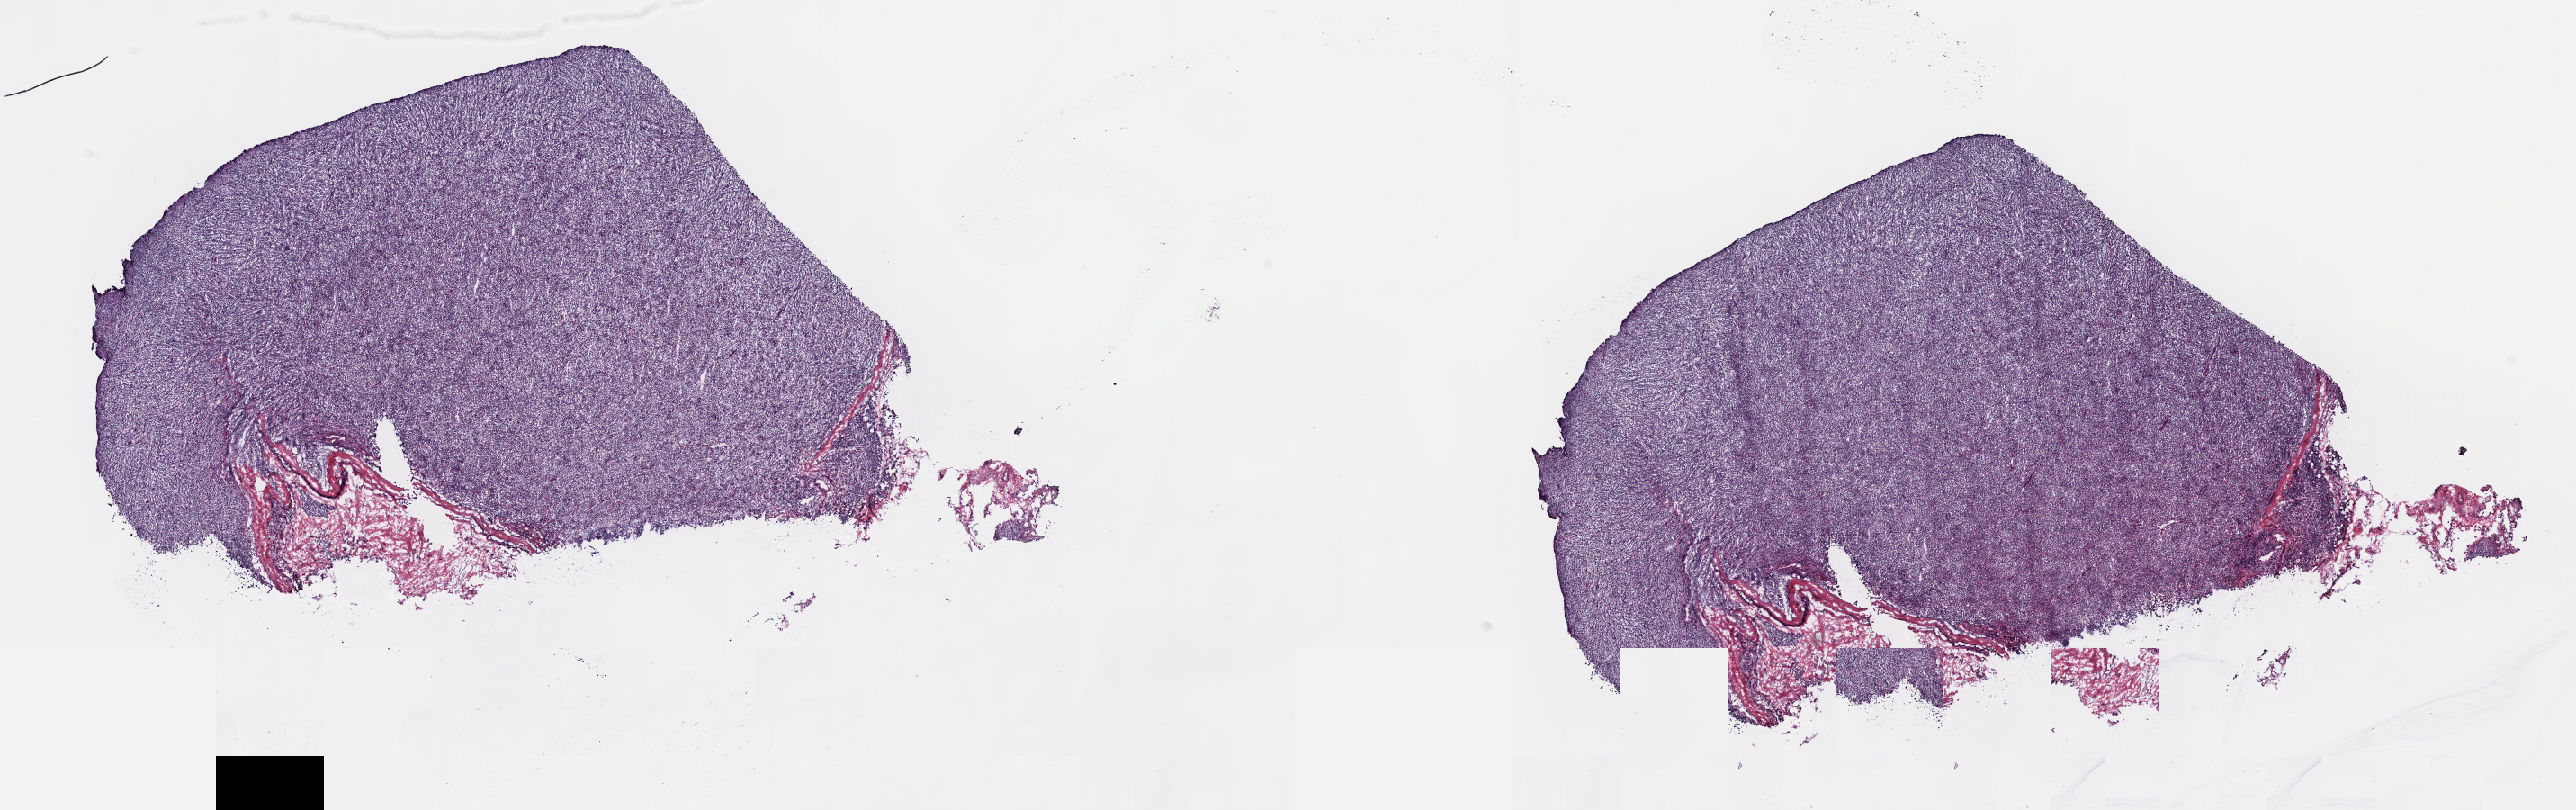
H&E-stained whole-slide image — low-resolution overview of the scanned area, about 23.2 x 7.3 mm; frozen section; primary tumour sample from the lymphoid tissue. Patient: female, age at initial diagnosis 40 years. Slide review estimates, as recorded: tumour cells 80%, tumour nuclei 90%, normal cells 0%, stromal cells 20%, necrosis 0%. Infiltration values recorded for this section: lymphocyte infiltration 85%, monocyte infiltration 5%, neutrophil infiltration 0%.
Pathologic diagnosis: Mediastinal (thymic) large B-cell lymphoma (lymph nodes of head, face and neck).